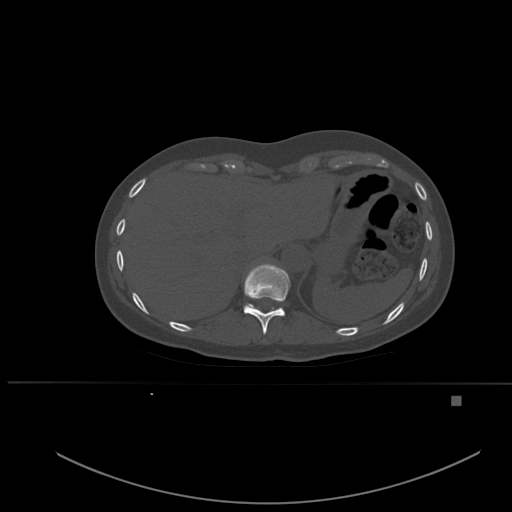
CT including the spine, one axial slice; slice 286 of 651 in the series (ordered by position); bone window (W 1800 / L 400 HU); 1.5 mm slice thickness; 512 × 512 image matrix. Patient: female, 49 years. From the clinical record (not read from this slice): primary cancer: breast; vertebrae with lytic lesions (as recorded): L3, T12, L4.
Annotated regions visible in this slice (semi-automatic segmentation, software-assisted and operator-edited):
- T10 vertebra: box from (x=243, y=264) to (x=290, y=335) px
- T11 vertebra: (x=250, y=304)–(x=255, y=309)